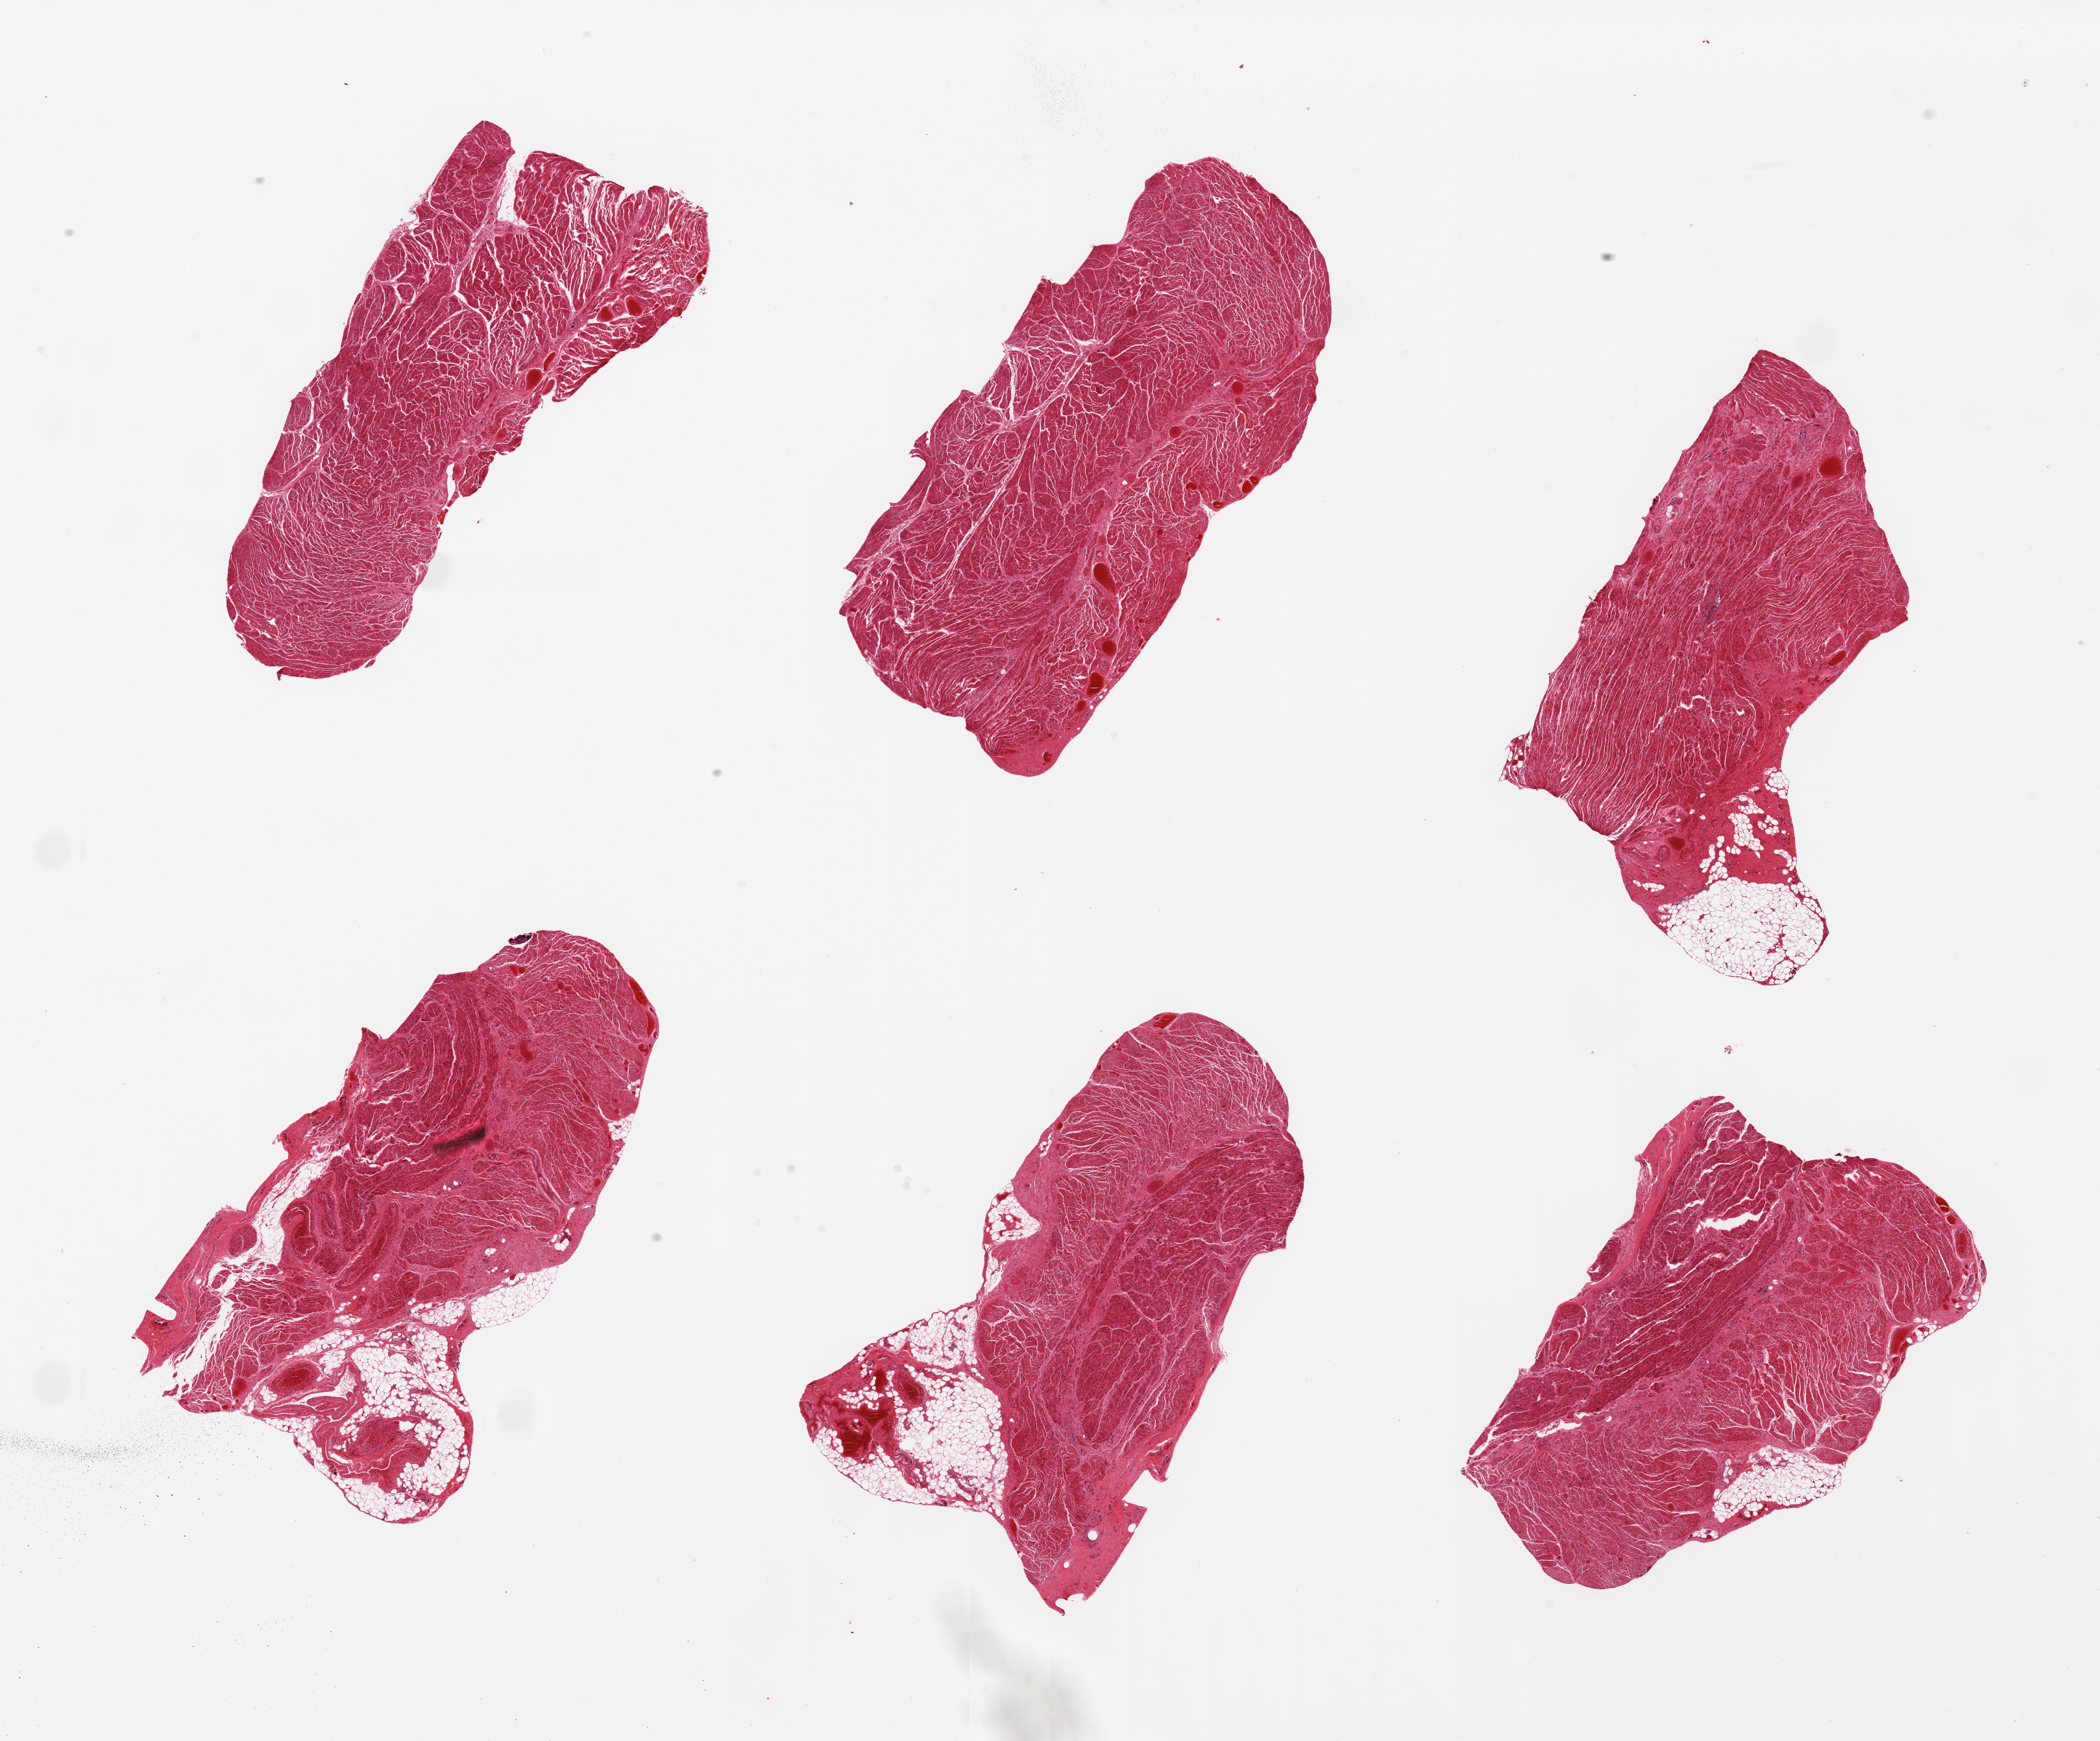
Whole-slide image, H&E stain — shown as a low-resolution overview of the whole scanned area (about 25.6 x 21.2 mm); PAXgene-fixed, paraffin-embedded tissue; section of gastroesophageal junction (target tissue); donor tissue sample. Donor: male.
Review note (as recorded): 6 pieces, some with residual attached fat.